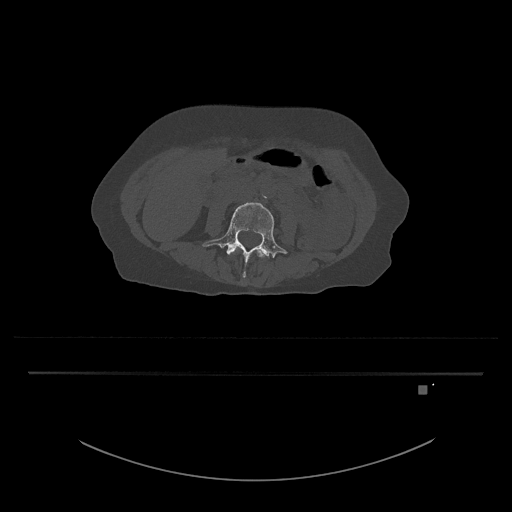
CT including the spine, one axial slice. Position 373 of 797 along the scan axis. 120 kVp. Bone window (W 1800 / L 400 HU). 0.5 mm slice thickness. 512 × 512 image matrix, field of view 500 × 500 mm. Female patient, age 57 years. From the clinical record (not read from this slice): primary cancer: cervical.
Outlined on this slice (semi-automatically segmented with operator editing):
- L3 vertebra: bounding box <257,250,265,257> (left, top, right, bottom; pixels)
- L4 vertebra: <202,202,287,278>